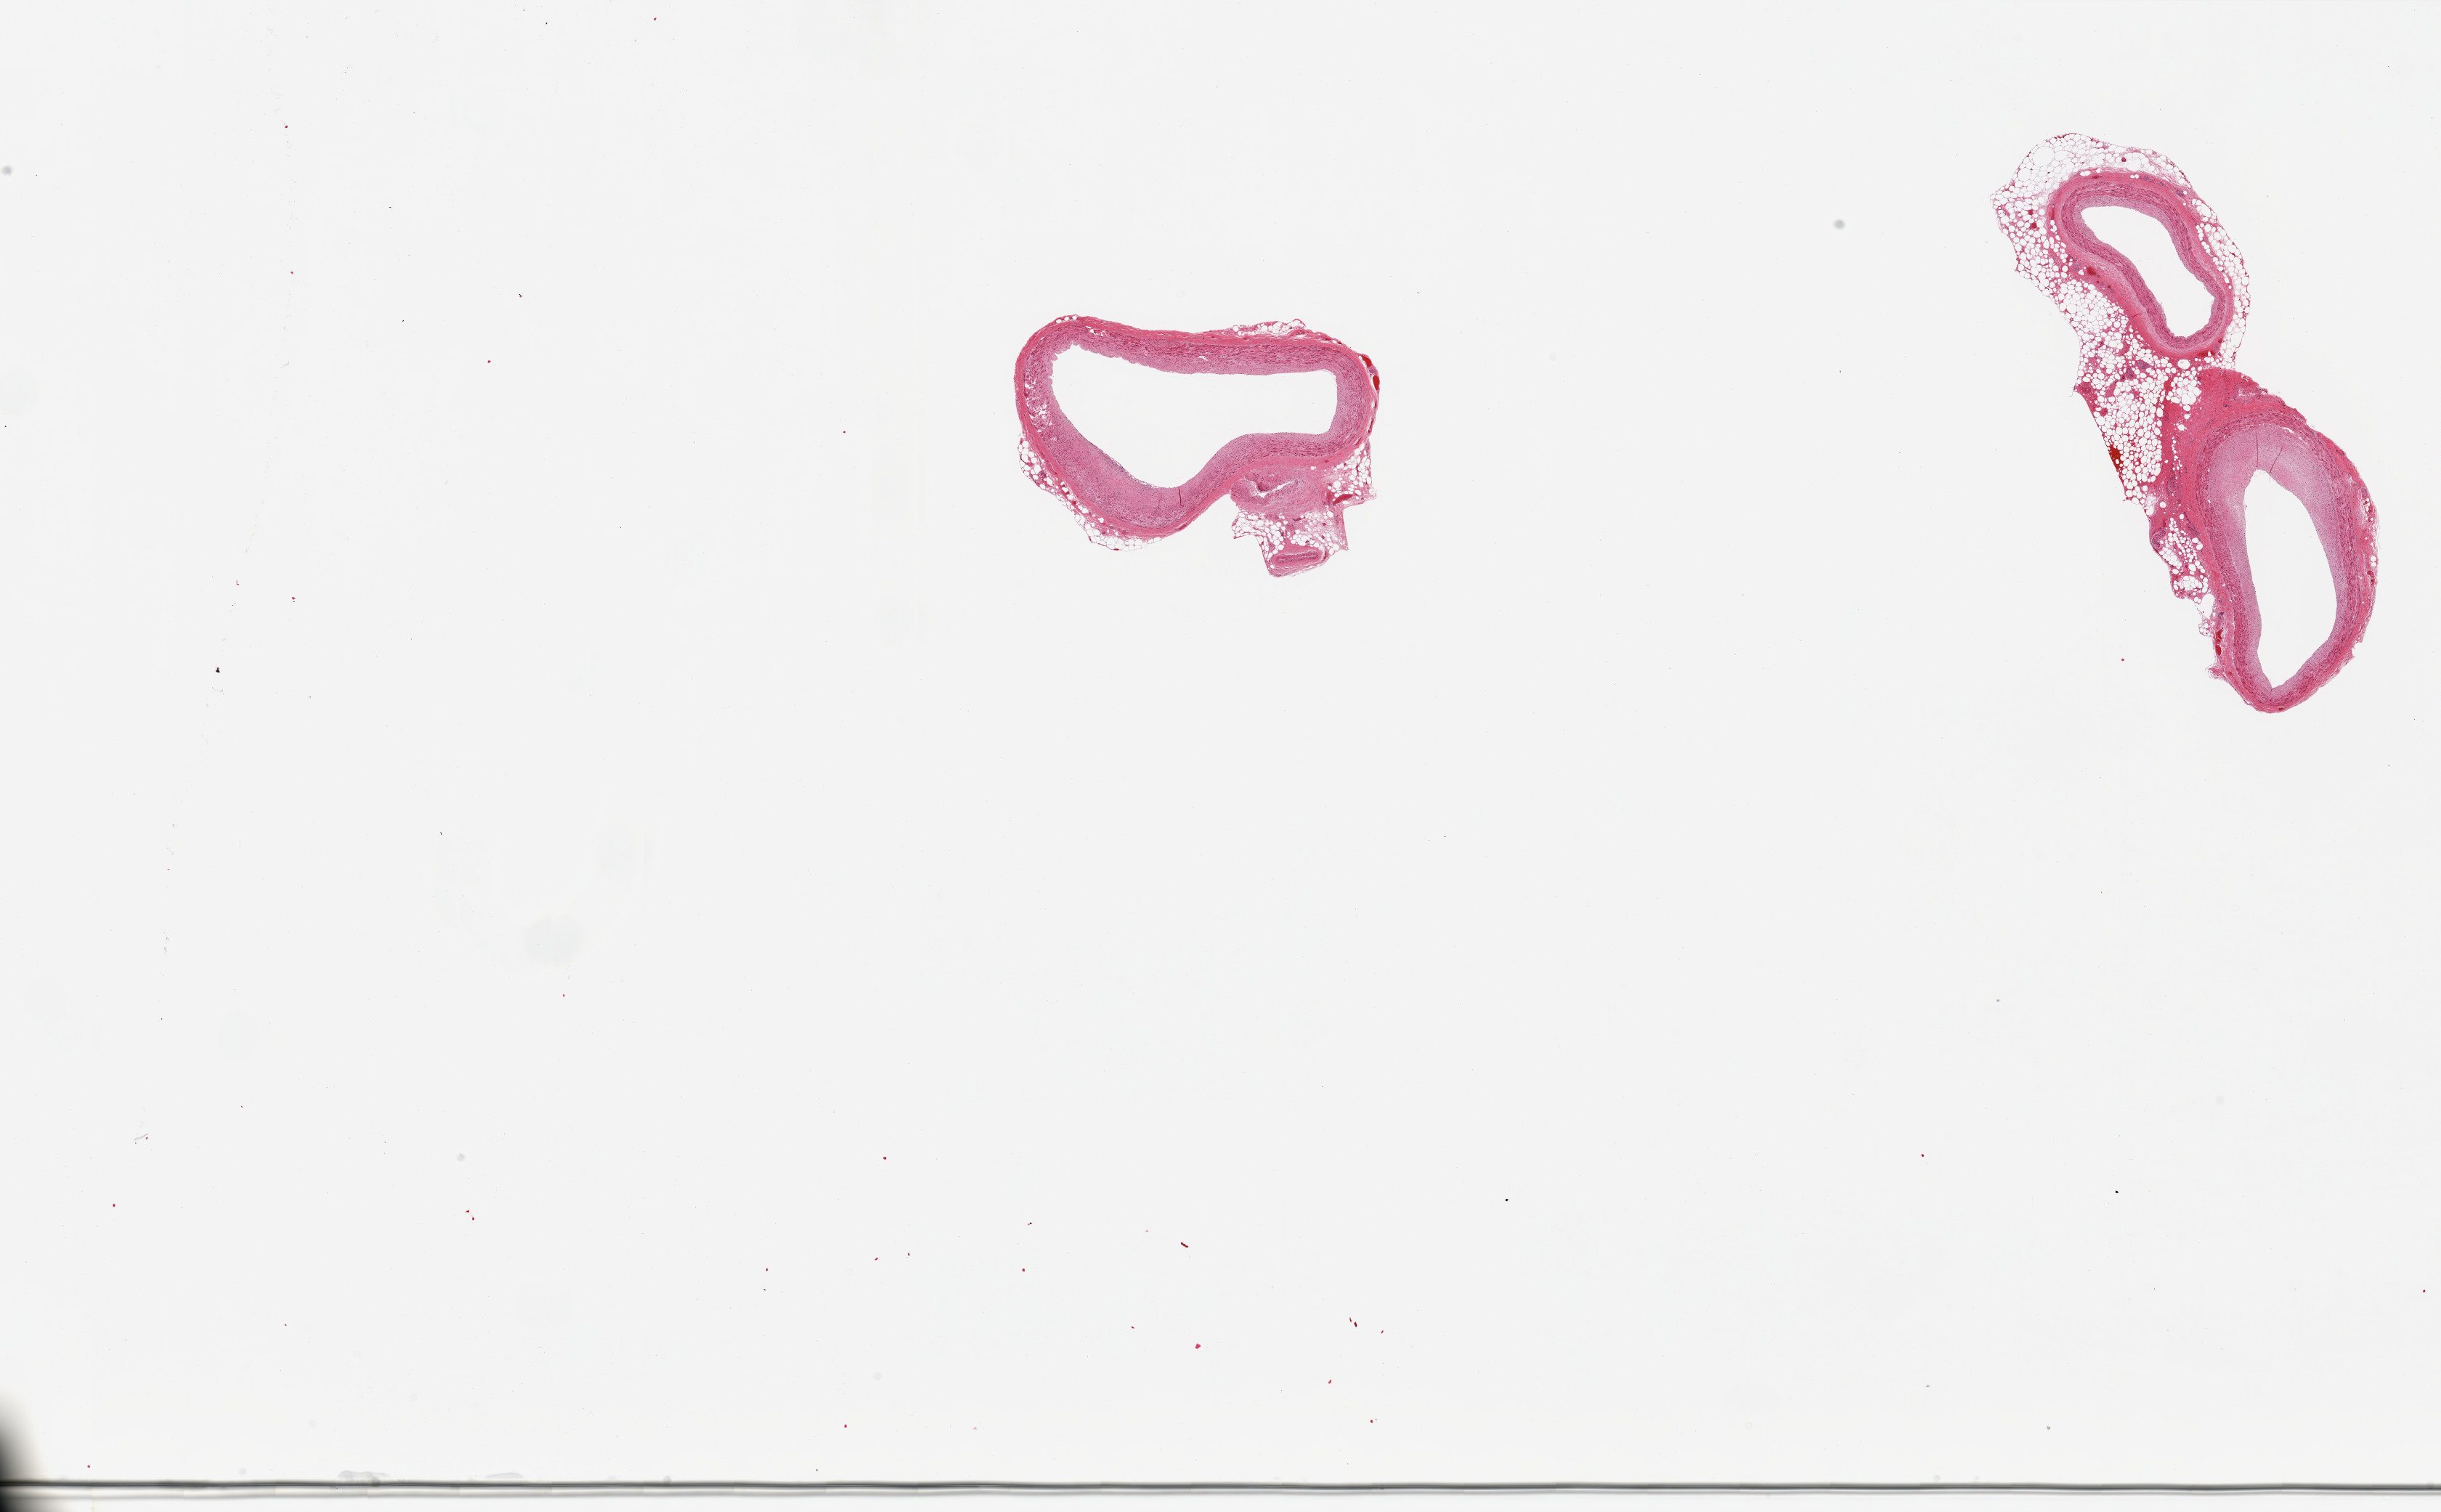
Whole-slide image, hematoxylin and eosin (H&E) stain, brightfield — low-resolution overview of the scanned area, about 26.6 x 16.5 mm (from a 20x scan), PAXgene-fixed paraffin-embedded (PFPE) section, section of coronary artery (target tissue), tissue donor sample. Female donor.
* review note (as recorded): 2 pieces; 3 vessels: 2 with plaque, 1 with 40% external fat